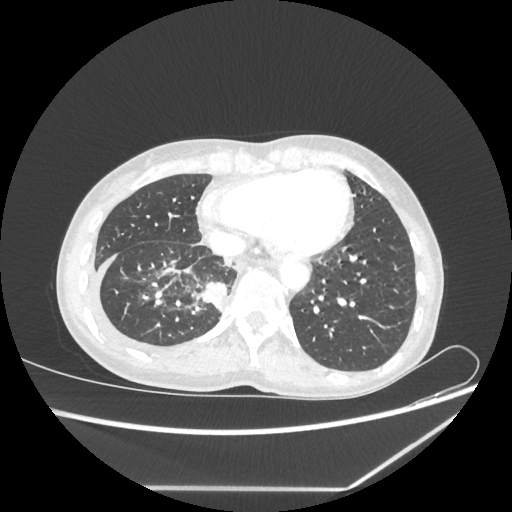
Chest CT, one axial slice; slice 69 of 237 in the series (ordered by position); reconstruction kernel STANDARD; 80 kVp; lung window (W 1500 / L -600 HU); 1.25 mm slice thickness; 512 × 512 image matrix, field of view 364 × 364 mm. Female patient, age 59 years. Case-level facts recorded for this patient, not image findings: clinical TNM (as recorded): T1c N1 M1.
Annotated regions visible in this slice (rectangle marked by the reading radiologist):
- lung tumour (recorded histology: adenocarcinoma): box from (x=200, y=279) to (x=229, y=315) px